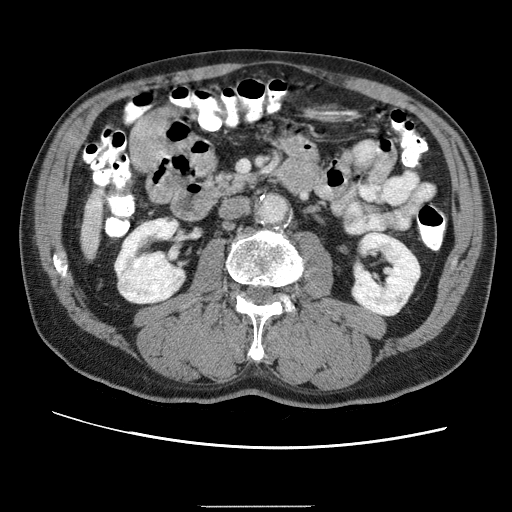
Contrast-enhanced abdominal CT (liver protocol), one axial slice. Position 3 of 75 along the scan axis. 120 kVp. One of 2 acquisitions stored at this slice position. Soft-tissue window (W 400 / L 40 HU). 2.5 mm slice thickness. 512 × 512 image matrix, field of view 360 × 360 mm. Case-level facts recorded for this patient, not image findings: diagnosis: hepatocellular carcinoma (patient treated with transarterial chemoembolisation; whether this scan precedes or follows treatment is not stated here); TNM stage (as recorded): Stage-II; Child-Pugh class: A; tumour differentiation: well differentiated; tumour nodularity: multinodular.
Structures marked on this image (semi-automatically segmented with operator editing):
- liver parenchyma outside the tumour (the mass and vessels are separate outlines, so this box may not span the whole liver): box from (x=90, y=238) to (x=101, y=250) px
- liver vessels: (x=91, y=238)–(x=101, y=250)